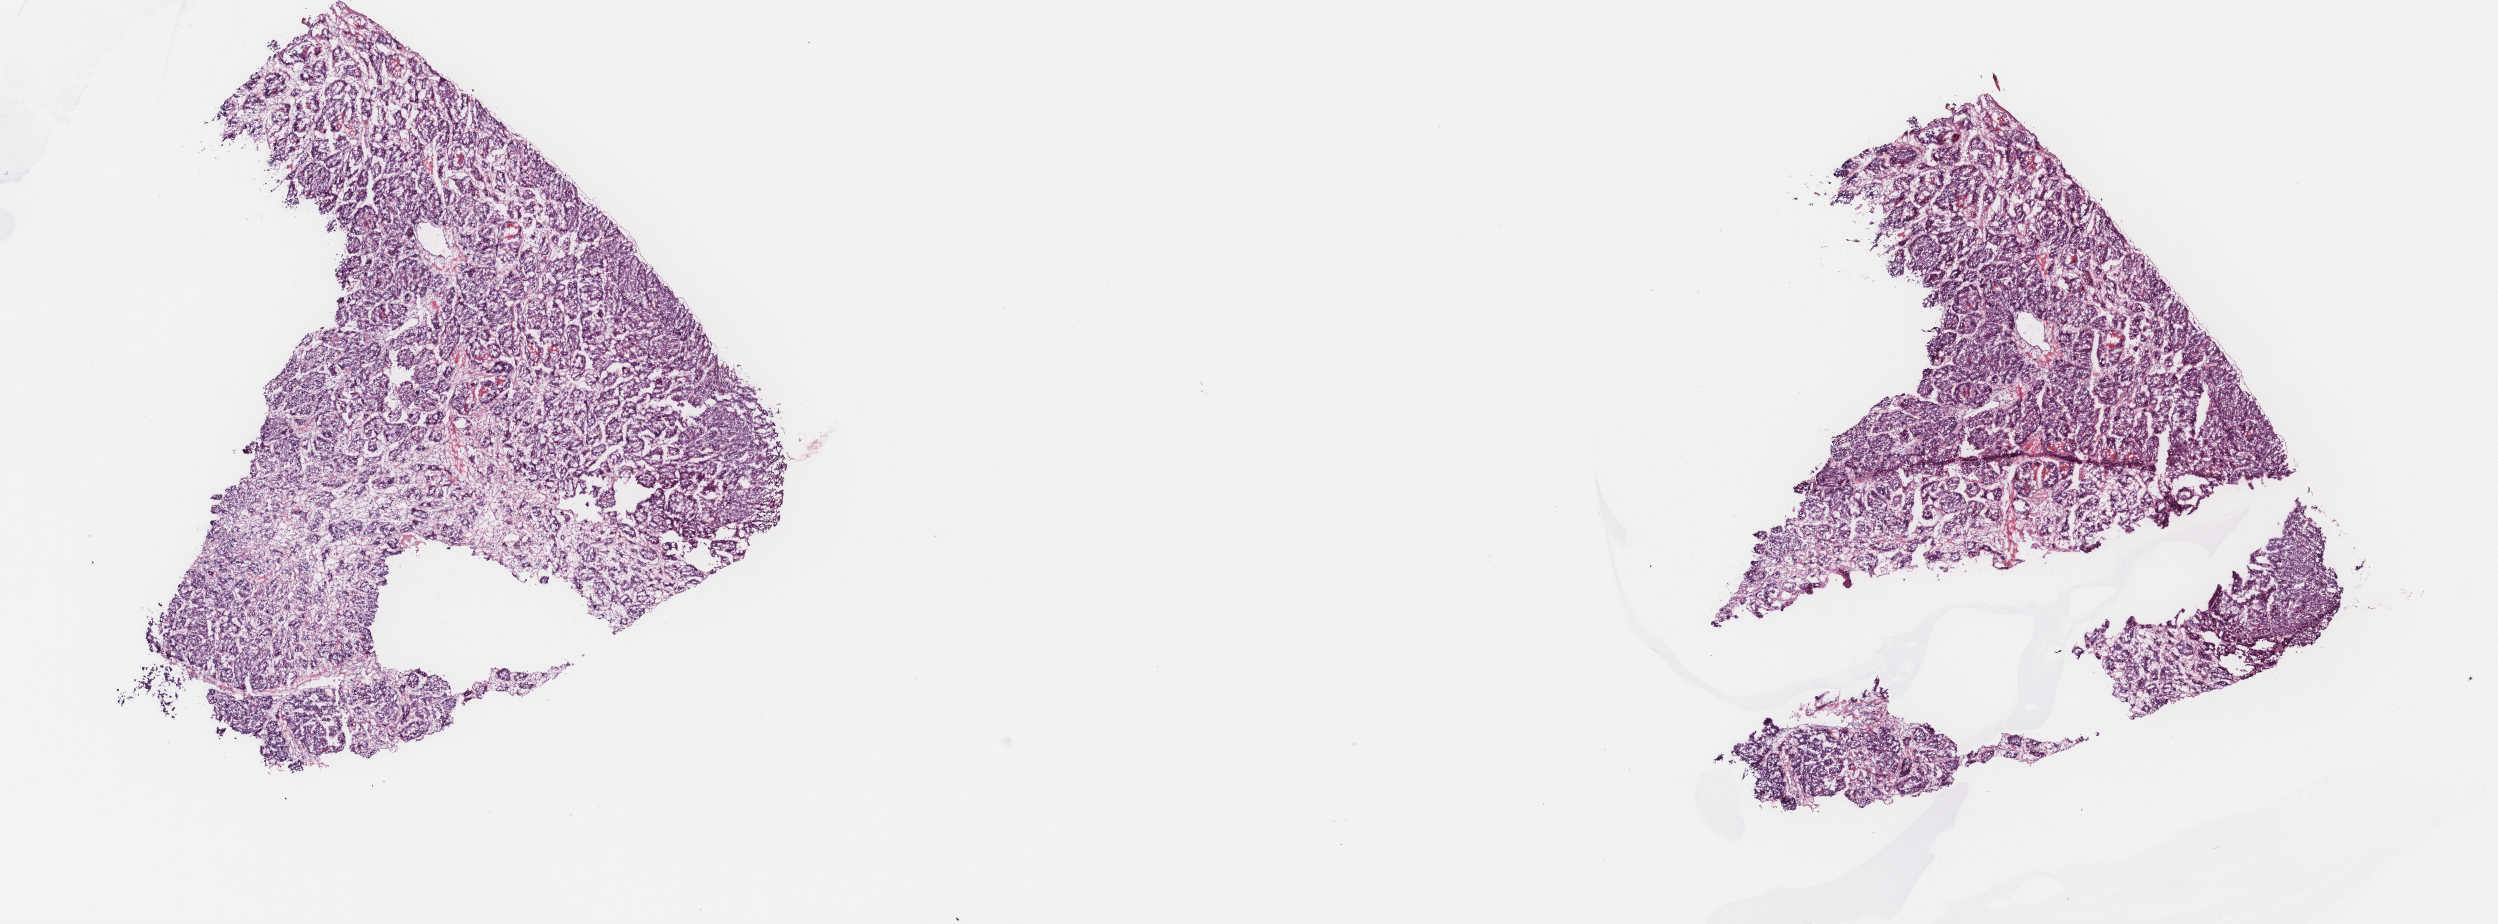
Whole-slide histology image, Hematoxylin and eosin (H&E) stained — low-resolution overview of the scanned area, about 19.8 x 7.3 mm, frozen section from the top of the tissue portion, primary tumour sample from the liver. Female patient; age at initial diagnosis 73 years.
Histologic diagnosis: Hepatocellular carcinoma, NOS.